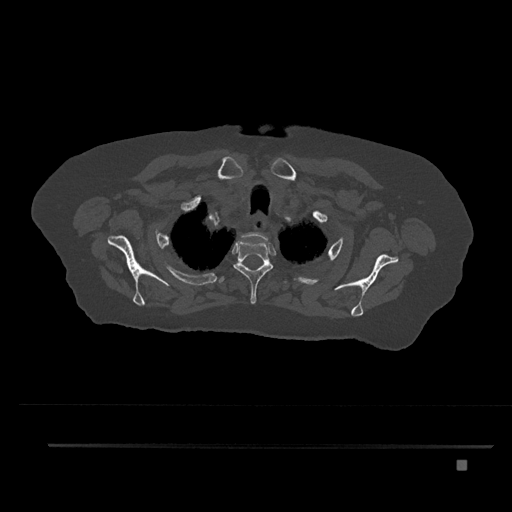
CT including the spine, one axial slice; position 667 of 797 along the scan axis; reconstruction kernel Br40s/3; bone window (W 1800 / L 400 HU); 0.5 mm slice thickness; 512 × 512 image matrix, field of view 437 × 437 mm. Patient: female, 76 years. From the clinical record (not read from this slice): primary cancer: lung.
Annotated regions visible in this slice (semi-automatic segmentation, software-assisted and operator-edited):
- T1 vertebra: bounding box <241,232,269,247> (left, top, right, bottom; pixels)
- T2 vertebra: <233,240,273,304>
- T3 vertebra: <220,277,286,283>